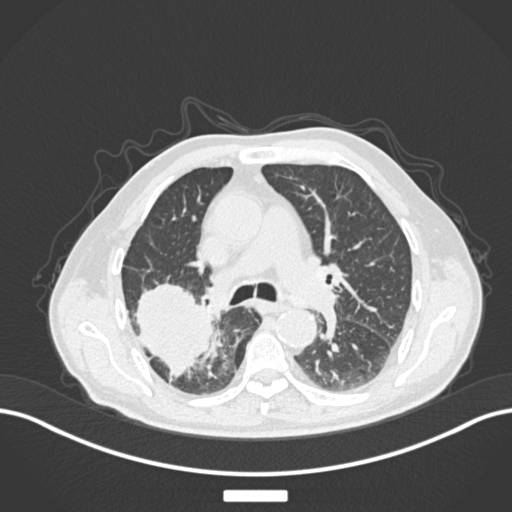
Chest CT, one axial slice; position 108 of 201 along the scan axis; 120 kVp; lung window (W 1500 / L -600 HU); 1 mm slice thickness; 512 × 512 image matrix. Male patient, age 72 years. Case-level facts recorded for this patient, not image findings: clinical TNM (as recorded): T3 N2 M0.
Structures marked on this image (rectangle marked by the reading radiologist):
- lung tumour (recorded histology: adenocarcinoma): box from (x=133, y=279) to (x=214, y=379) px